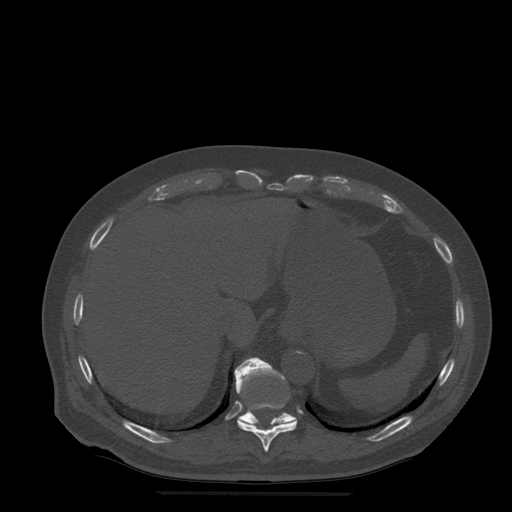
CT including the spine, one axial slice. Position 260 of 522 along the scan axis. Bone window (W 1800 / L 400 HU). 1.25 mm slice thickness. 512 × 512 image matrix. Patient age 72 years. From the clinical record (not read from this slice): primary cancer: prostate.
Outlined on this slice (semi-automatically segmented with operator editing):
- T10 vertebra: box from (x=237, y=368) to (x=297, y=452) px
- T11 vertebra: (x=235, y=358)–(x=297, y=426)